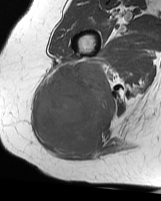
MRI of an extremity soft-tissue mass, one axial slice. Slice 36 of 70 in the series (ordered by position). MR volume resampled by the dataset authors to the PET/CT grid (not the native acquisition matrix). 3.27 mm slice thickness. 161 × 201 image matrix. Female patient. Case-level facts recorded for this patient, not image findings: histological type: synovial sarcoma; grade: intermediate; site of the primary tumour: right buttock.
Outlined on this slice (expert contour drawn on MRI and transferred to this co-registered scan by the dataset authors):
- gross tumour volume including surrounding oedema: bounding box <37,61,116,155> (left, top, right, bottom; pixels)
- gross tumour volume (mass): <37,61,116,155>